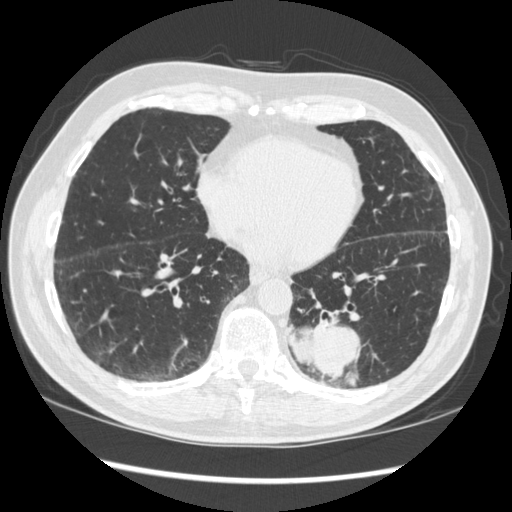
Axial slice from a low-dose chest CT screening exam; baseline screening round; lung window (W 1500 / L -600 HU); standard (soft-tissue) reconstruction kernel (STANDARD); 512 × 512 image matrix, field of view 360 × 360 mm. Male, age 72 years at enrolment. Current smoker at enrolment.
- Expert-annotated lung lesion, bounding box [x1, y1, x2, y2] px = [273, 296, 377, 384].
- The screening reader recorded 2 non-calcified nodules or masses ≥4 mm on this exam (left lower lobe, right middle lobe); which of them this box marks is not recorded.
- Official screen result: positive, change unspecified: nodule(s) >= 4 mm or enlarging nodule(s), mass(es), or other non-specific abnormalities suspicious for lung cancer.
- Participant outcome: lung cancer diagnosed 37 days after this screen — squamous cell carcinoma, NOS, left lower lobe, stage IIIA (AJCC 6th edition), 60 mm at pathology.